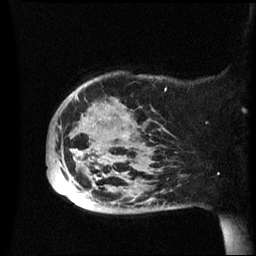
Breast MRI (dynamic contrast-enhanced), one sagittal slice; slice 12 of 60 in the series (ordered by position); dynamic contrast-enhanced series, image 2 of 3 at this slice position (ordered by acquisition); 1.5 T; TE 4.2 ms, TR 8.4 ms; 2.4 mm slice thickness; 256 × 256 image matrix, field of view 230 × 230 mm. Patient: female, 49 years.
Structures marked on this image (semi-automatically segmented with operator editing):
- analysis volume of interest (the breast-tissue region the enhancement analysis was run in; not a lesion): bounding box <47,72,174,214> (left, top, right, bottom; pixels)
- tumour enhancement mask (voxels above the 70 % enhancement threshold inside the analysis volume of interest): <59,166,73,195>